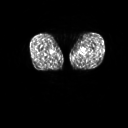
FDG PET of an extremity soft-tissue mass (from a PET/CT study), one axial slice; slice 4 of 267 in the series (ordered by position); 128 × 128 image matrix, field of view 600 × 600 mm. Patient: male, 59 years. From the clinical record (not read from this slice): histological type: pleiomorphic liposarcoma; grade: high; site of the primary tumour: left thigh.
Annotated regions visible in this slice (expert contour drawn on MRI and transferred to this co-registered scan by the dataset authors):
- gross tumour volume including surrounding oedema: box from (x=82, y=54) to (x=86, y=57) px